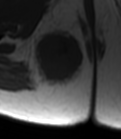
MRI of an extremity soft-tissue mass, one axial slice. Slice 24 of 47 in the series (ordered by position). MR volume resampled by the dataset authors to the PET/CT grid (not the native acquisition matrix). 3.27 mm slice thickness. 121 × 139 image matrix, field of view 118 × 136 mm. Female patient. Case-level facts recorded for this patient, not image findings: histological type: epithelioid sarcoma; grade: intermediate; site of the primary tumour: right buttock.
Structures marked on this image (expert contour drawn on MRI and transferred to this co-registered scan by the dataset authors):
- gross tumour volume including surrounding oedema: bounding box (x1, y1, x2, y2) in pixels: (31, 27, 83, 87)
- gross tumour volume (mass): (34, 32, 83, 83)